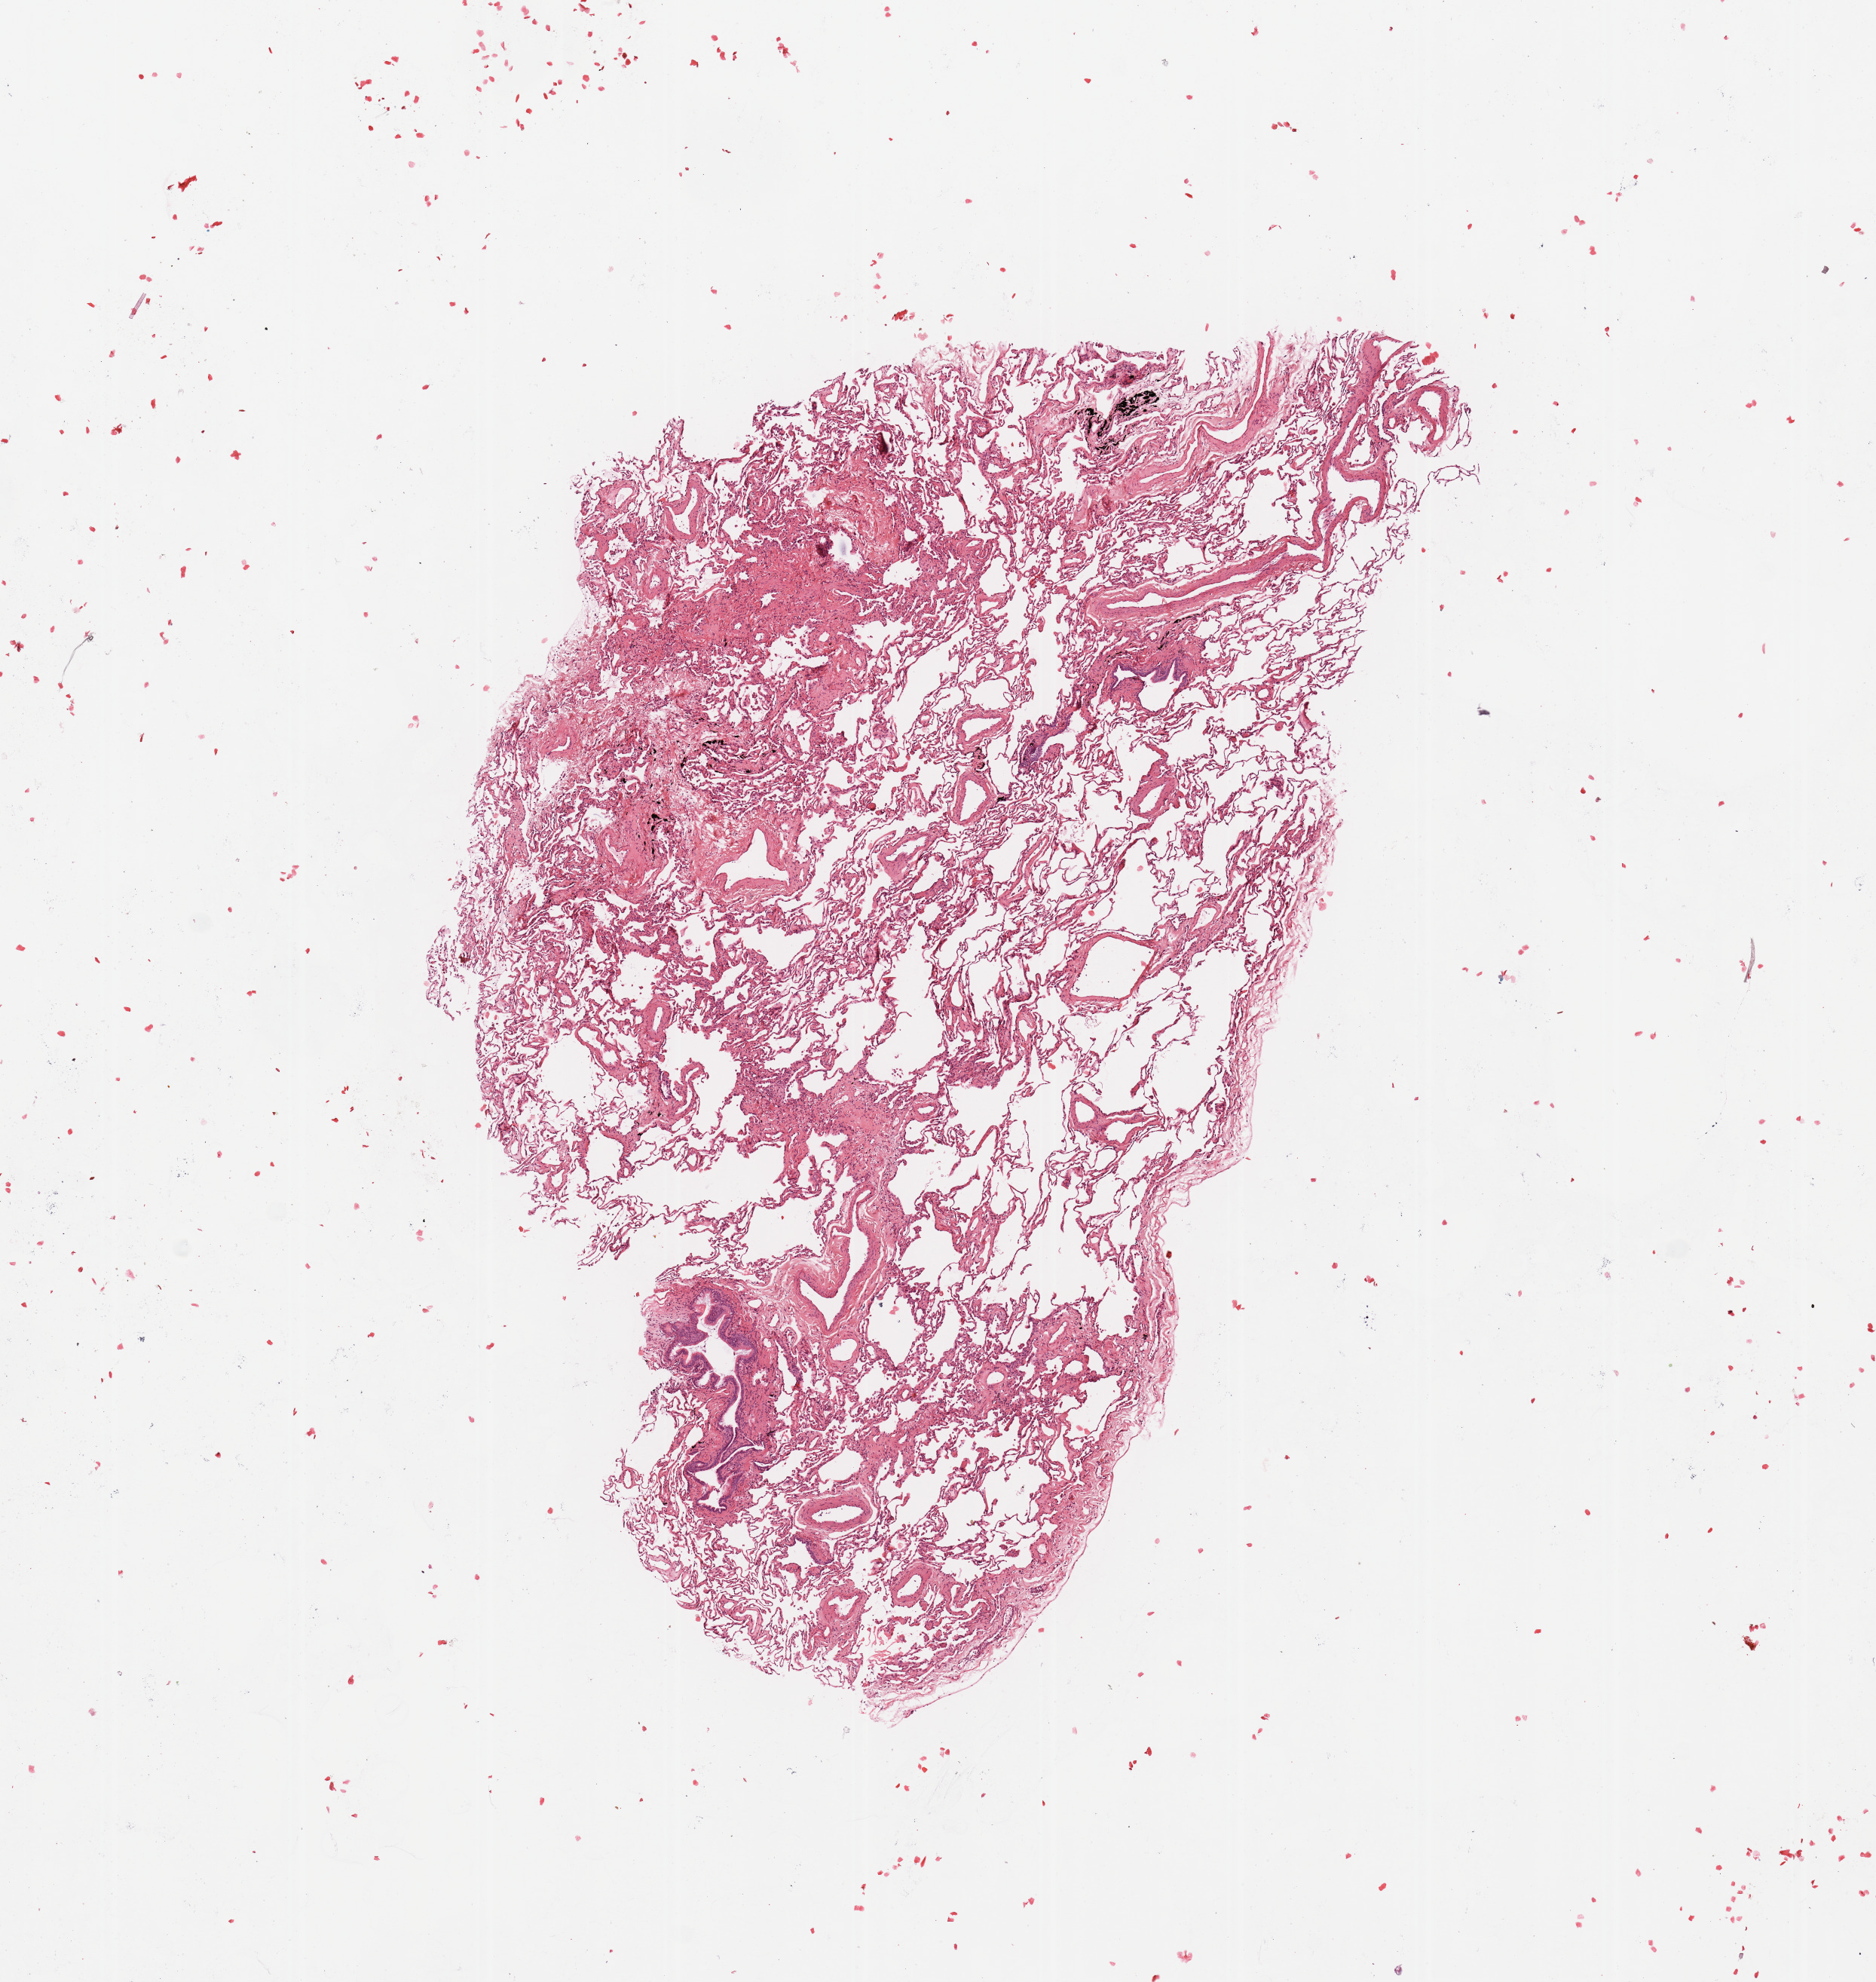
Whole-slide histology image, Hematoxylin and eosin (H&E) stained, a low-resolution overview of the entire scanned area, about 9.8 x 10.4 mm; normal (non-tumour) tissue sample, sampled site: lung. 72-year-old female patient.
- this section: normal (non-tumour) tissue from the same patient
- patient diagnosis: Squamous cell carcinoma, NOS